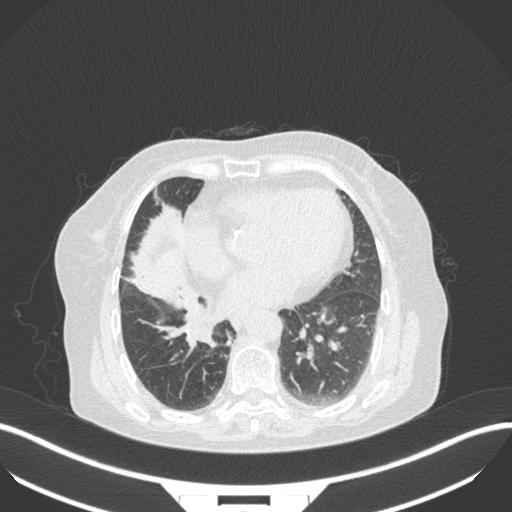
Chest CT, one axial slice; slice 120 of 329 in the series (ordered by position); 120 kVp; lung window (W 1500 / L -600 HU); 1 mm slice thickness; 512 × 512 image matrix, field of view 400 × 400 mm. Female patient, age 75 years. Case-level facts recorded for this patient, not image findings: clinical TNM (as recorded): T1b N0 M1a.
Outlined on this slice (bounding box drawn by a radiologist):
- lung tumour (recorded histology: squamous cell carcinoma): bounding box (x1, y1, x2, y2) in pixels: (178, 305, 217, 347)